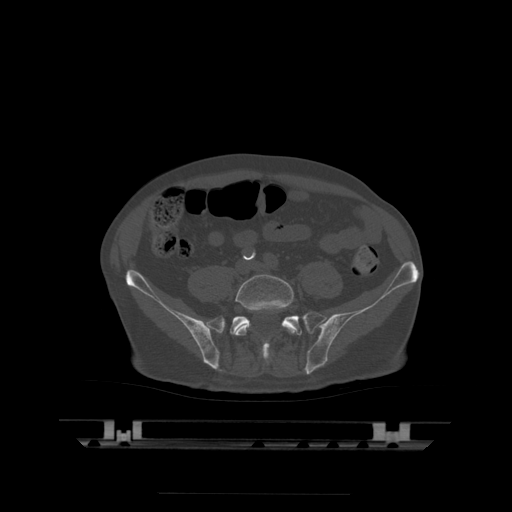
CT including the spine, one axial slice. Position 65 of 522 along the scan axis. Bone window (W 1800 / L 400 HU). 1.25 mm slice thickness. 512 × 512 image matrix, field of view 436 × 436 mm. Patient age 68 years. From the clinical record (not read from this slice): primary cancer: urothelial.
Annotated regions visible in this slice (semi-automatically segmented with operator editing):
- L5 vertebra: box from (x=235, y=275) to (x=295, y=354) px